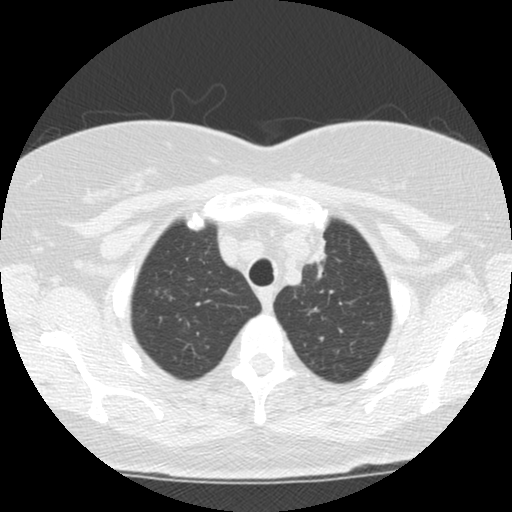
Low-dose screening chest CT, one axial slice. Position 100 of 120 along the scan axis. 120 kVp. Lung window (W 1500 / L -600 HU). 2.5 mm slice thickness. 512 × 512 image matrix.
Structures marked on this image (outlined manually by an expert reader):
- lesion 1 (tumor, upper lobe of left lung): bounding box <307,241,326,264> (left, top, right, bottom; pixels)